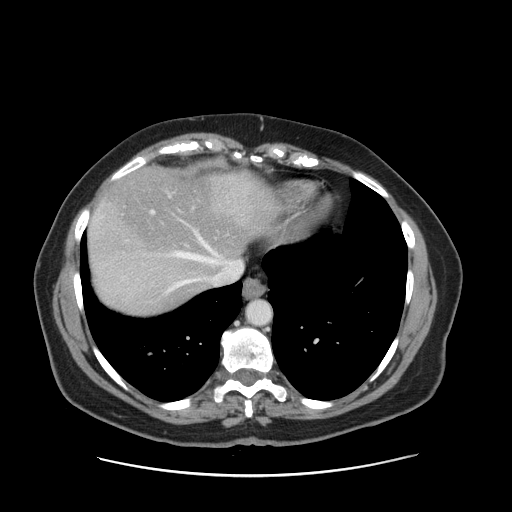
Contrast-enhanced abdominal CT, one axial slice. Position 133 of 161 along the scan axis. 120 kVp. Intravenous contrast given. Soft-tissue window (W 400 / L 40 HU). 2.5 mm slice thickness. 512 × 512 image matrix, field of view 398 × 398 mm. Female patient, age 62 years. From the clinical record (not read from this slice): diagnosis: colorectal cancer liver metastases, imaged before liver resection; multiple liver metastases: no; largest metastasis: 2.5 cm; chemotherapy before resection: yes.
Outlined on this slice (expert manual segmentation):
- hepatic veins: bounding box [x1, y1, x2, y2] px = [123, 187, 243, 293]
- liver: [89, 168, 278, 314]
- planned liver remnant (the part of the liver to remain after resection): [95, 168, 277, 277]
- portal vein (with intrahepatic branches): [151, 190, 181, 214]